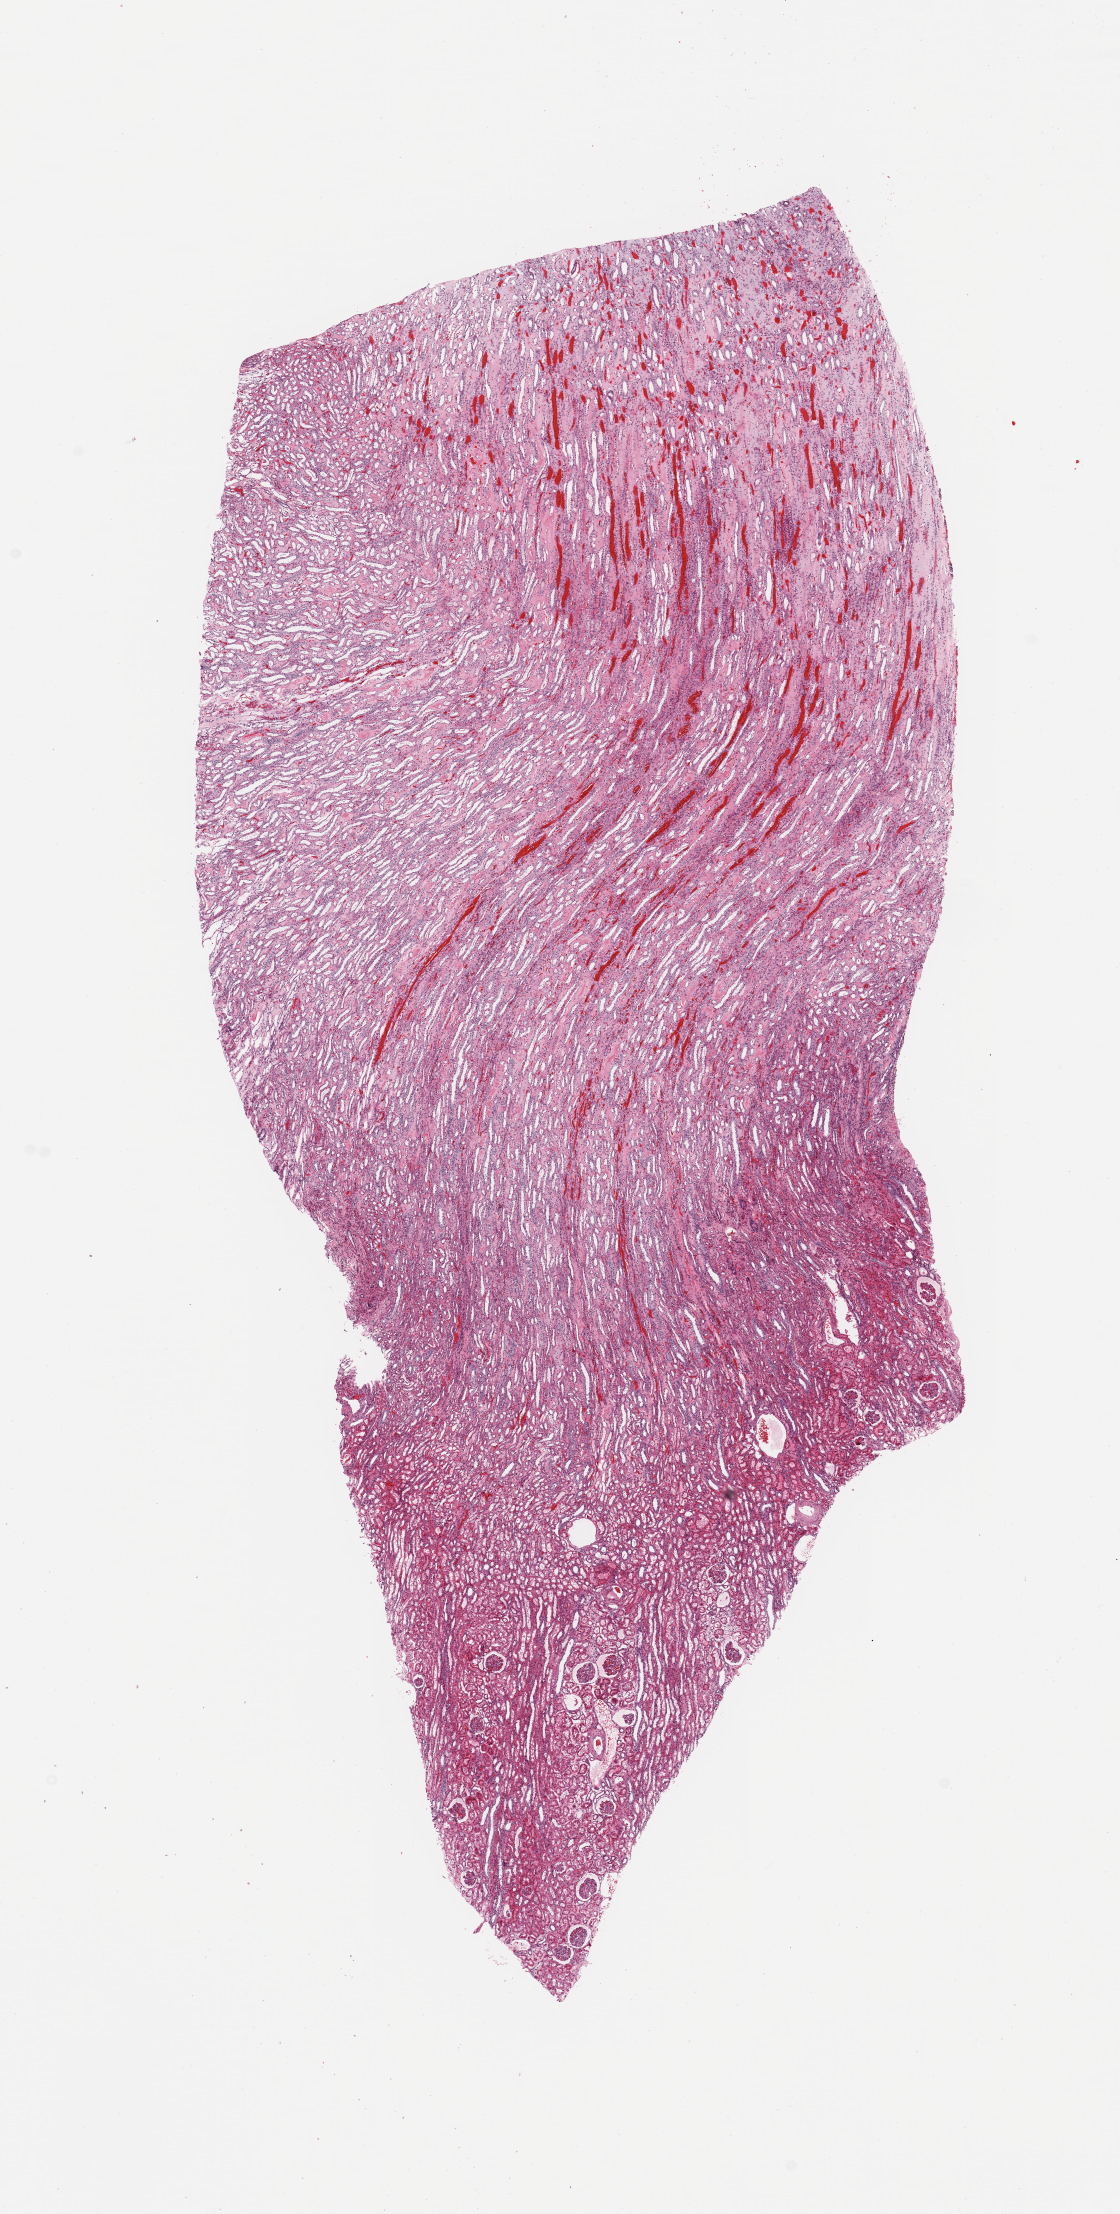
Whole-slide histology image, H&E, low-resolution overview of the scanned area, about 8.9 x 17.5 mm; normal (non-tumour) tissue sample, sampled site: kidney. Male, 72 y/o.
This section: normal (non-tumour) tissue from the same patient. Patient diagnosis: Renal cell carcinoma, NOS.